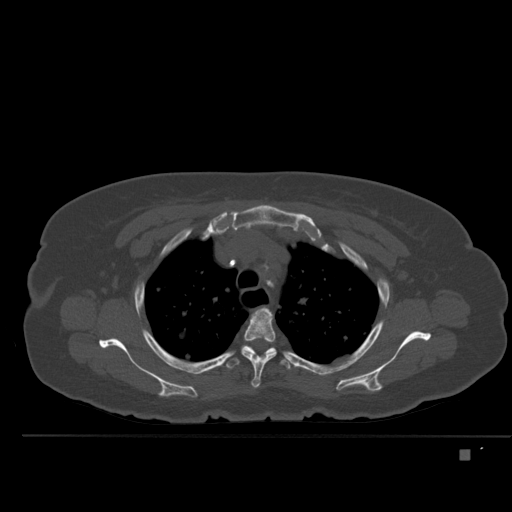
CT including the spine, one axial slice; position 376 of 477 along the scan axis; bone window (W 1800 / L 400 HU); 1.5 mm slice thickness; 512 × 512 image matrix, field of view 422 × 422 mm. Female patient, age 74 years. From the clinical record (not read from this slice): primary cancer: colon.
Structures marked on this image (semi-automatically segmented with operator editing):
- T3 vertebra: bounding box [x1, y1, x2, y2] px = [241, 308, 277, 388]
- T4 vertebra: [225, 345, 292, 370]